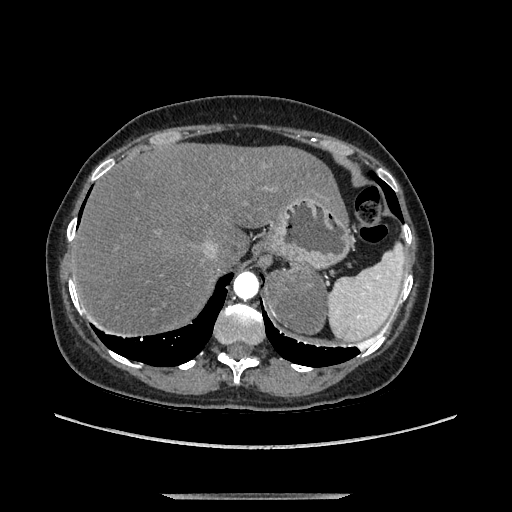
Contrast-enhanced abdominal CT, one axial slice; slice 109 of 169 in the series (ordered by position); soft-tissue window (W 400 / L 40 HU); 1.25 mm slice thickness; 512 × 512 image matrix, field of view 400 × 400 mm. Female patient. From the clinical record (not read from this slice): diagnosis: adrenocortical carcinoma; tumour side: left adrenal; tumour size at pathology: 9 cm; Ki-67 index: 2 %; stage (as recorded): 3.
Structures marked on this image (semi-automatically segmented with operator editing):
- mass: bounding box <272,264,325,330> (left, top, right, bottom; pixels)